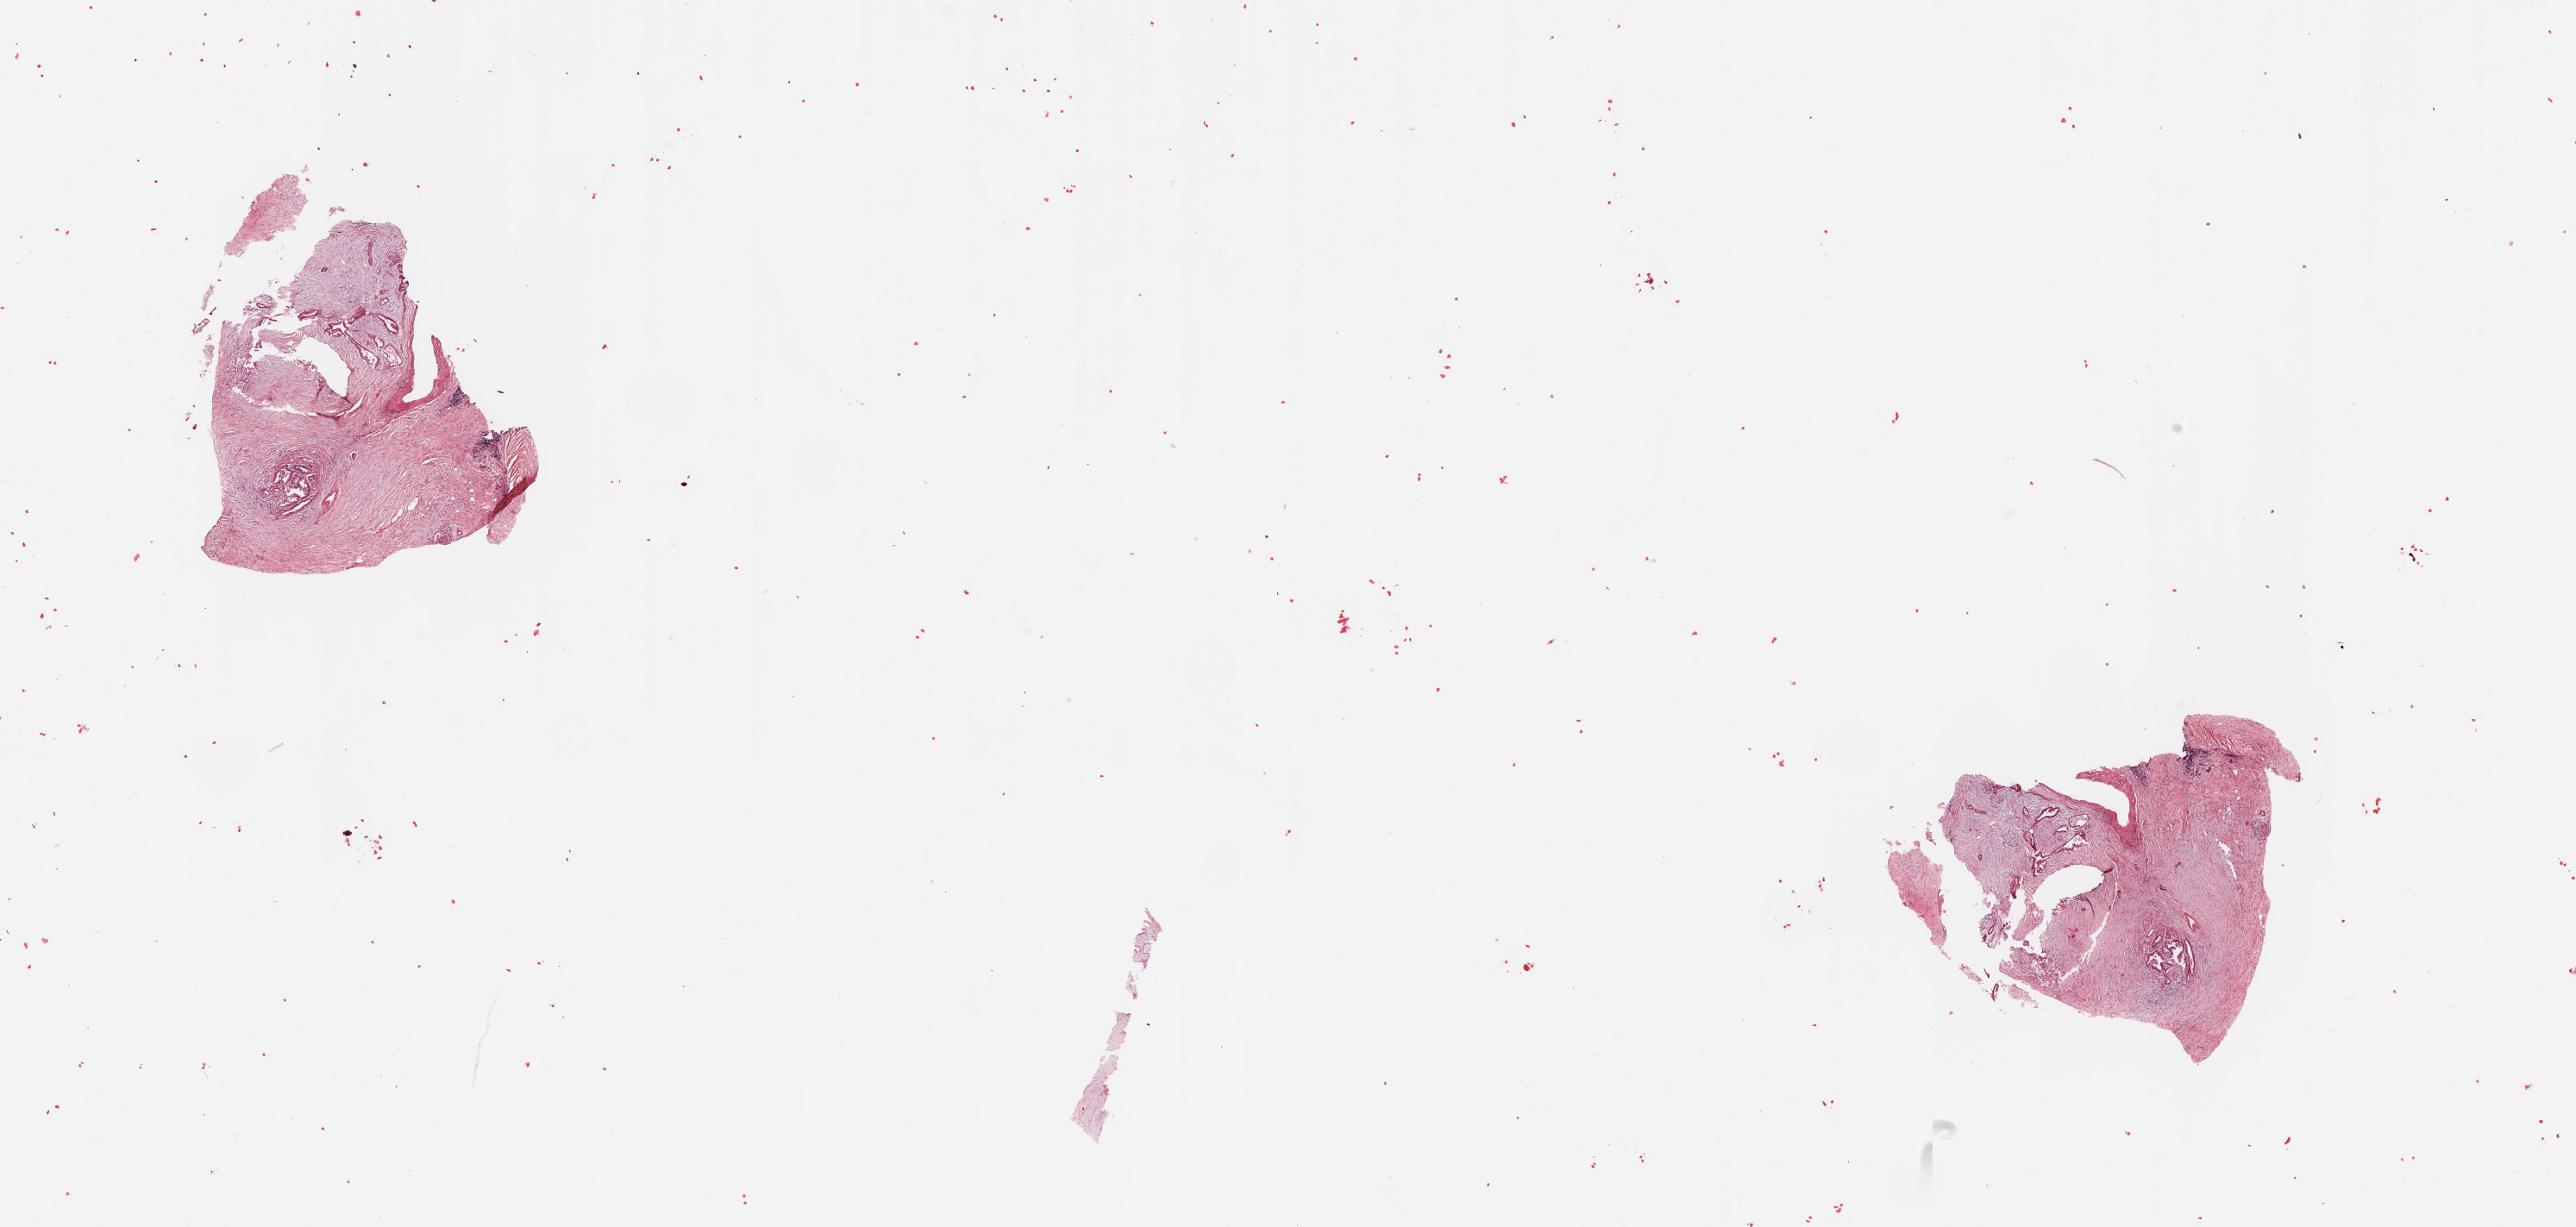
Whole-slide histology image, Hematoxylin and eosin (H&E) stained, shown as a low-resolution overview of the whole scanned area (about 23.6 x 11.3 mm, slide scanned at 20x), pancreas, tumour tissue. 45-year-old female patient.
Diagnosis: Infiltrating duct carcinoma, NOS.